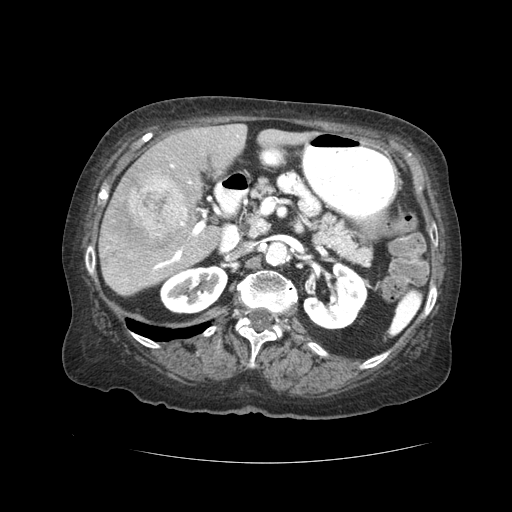
Contrast-enhanced abdominal CT (liver protocol), one axial slice; position 15 of 59 along the scan axis; reconstruction kernel STANDARD; 120 kVp; soft-tissue window (W 400 / L 40 HU); 512 × 512 image matrix. Case-level facts recorded for this patient, not image findings: diagnosis: hepatocellular carcinoma (patient treated with transarterial chemoembolisation; whether this scan precedes or follows treatment is not stated here); TNM stage (as recorded): Stage-I; Child-Pugh class: A.
Structures marked on this image (semi-automatic segmentation, software-assisted and operator-edited):
- liver parenchyma outside the tumour (the mass and vessels are separate outlines, so this box may not span the whole liver): bounding box <98,124,309,296> (left, top, right, bottom; pixels)
- mass: <130,175,186,237>
- liver vessels: <153,135,238,270>